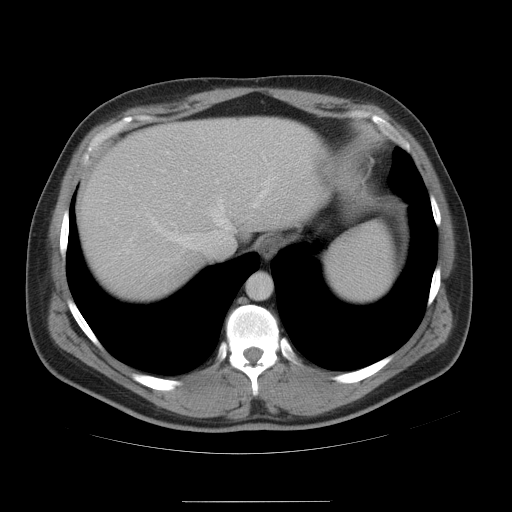
Contrast-enhanced abdominal CT, one axial slice; slice 43 of 54 in the series (ordered by position); 120 kVp; intravenous contrast given; soft-tissue window (W 400 / L 40 HU); 5 mm slice thickness; 512 × 512 image matrix. Male patient, age 40 years. Case-level facts recorded for this patient, not image findings: diagnosis: colorectal cancer liver metastases, imaged before liver resection; multiple liver metastases: no; largest metastasis: 15 cm; disease in both lobes: no.
Annotated regions visible in this slice (outlined manually by an expert reader):
- hepatic veins: bounding box <129,176,276,249> (left, top, right, bottom; pixels)
- liver: <77,118,330,303>
- planned liver remnant (the part of the liver to remain after resection): <165,118,331,264>